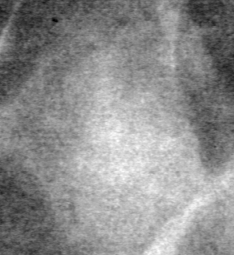
Cropped region of a digitized screen-film mammogram centred on a radiologist-marked abnormality, left breast, CC view, BI-RADS breast density category 2 (scale 1–4).
Finding: mass, shape oval, margins ill defined; BI-RADS assessment category 4; pathology (as recorded): benign.